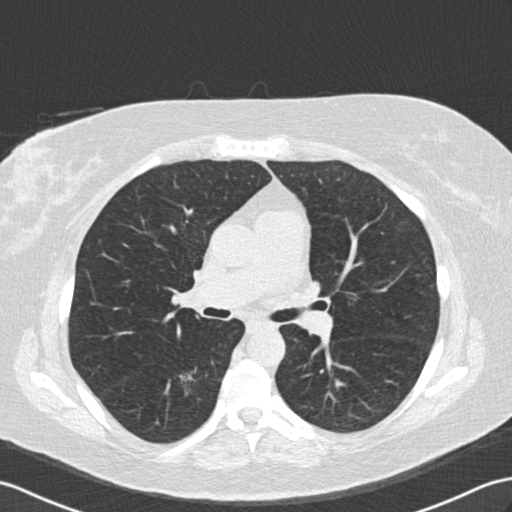
Axial slice from a low-dose chest CT screening exam, second annual screen, lung window (W 1500 / L -600 HU), 2 mm slice thickness, 120 kVp, slice 63 of 154 in the series. Female, age 65 years at enrolment. Former smoker at enrolment.
Lesion marked by an expert reader, bounding box (x1, y1, x2, y2) in pixels: (157, 354, 214, 411). Screening reader's record for this exam (one nodule recorded; not confirmed to be the boxed lesion): non-calcified nodule or mass ≥4 mm, right lower lobe, 18 × 16 mm, spiculated (stellate) margins, soft tissue attenuation, pre-existing on the prior screen: yes; interval growth: yes. Lung cancer was diagnosed 239 days after this screen: adenocarcinoma, NOS, right lower lobe, moderately differentiated (G2), stage IA (AJCC 6th edition), 25 mm at pathology.